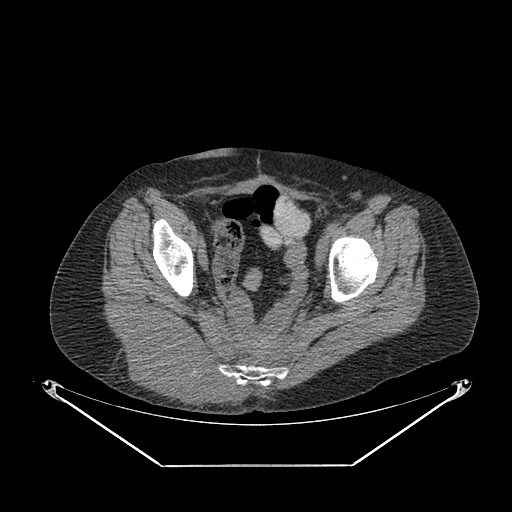
CT of an extremity soft-tissue mass (from a PET/CT study), one axial slice; position 62 of 267 along the scan axis; soft-tissue window (W 400 / L 40 HU); 3.75 mm slice thickness; 512 × 512 image matrix. Female patient. Case-level facts recorded for this patient, not image findings: histological type: spindle cell suggestive of myxofibrosarcoma; grade: intermediate; site of the primary tumour: right buttock.
Structures marked on this image (expert contour drawn on MRI and transferred to this co-registered scan by the dataset authors):
- gross tumour volume (mass): bounding box (x1, y1, x2, y2) in pixels: (117, 319, 241, 405)